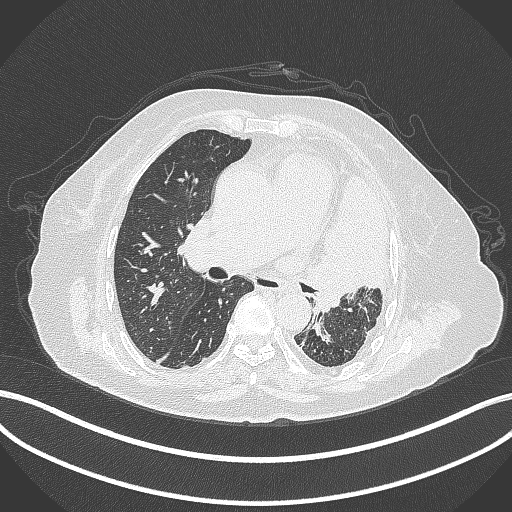
Chest CT, one axial slice; position 213 of 399 along the scan axis; reconstruction kernel B70f; 120 kVp; lung window (W 1500 / L -600 HU); 512 × 512 image matrix, field of view 400 × 400 mm. Patient: female, 75 years. Case-level facts recorded for this patient, not image findings: clinical TNM (as recorded): T3 N3 M1.
Outlined on this slice (bounding box drawn by a radiologist):
- lung tumour (recorded histology: adenocarcinoma): box from (x=306, y=175) to (x=390, y=319) px